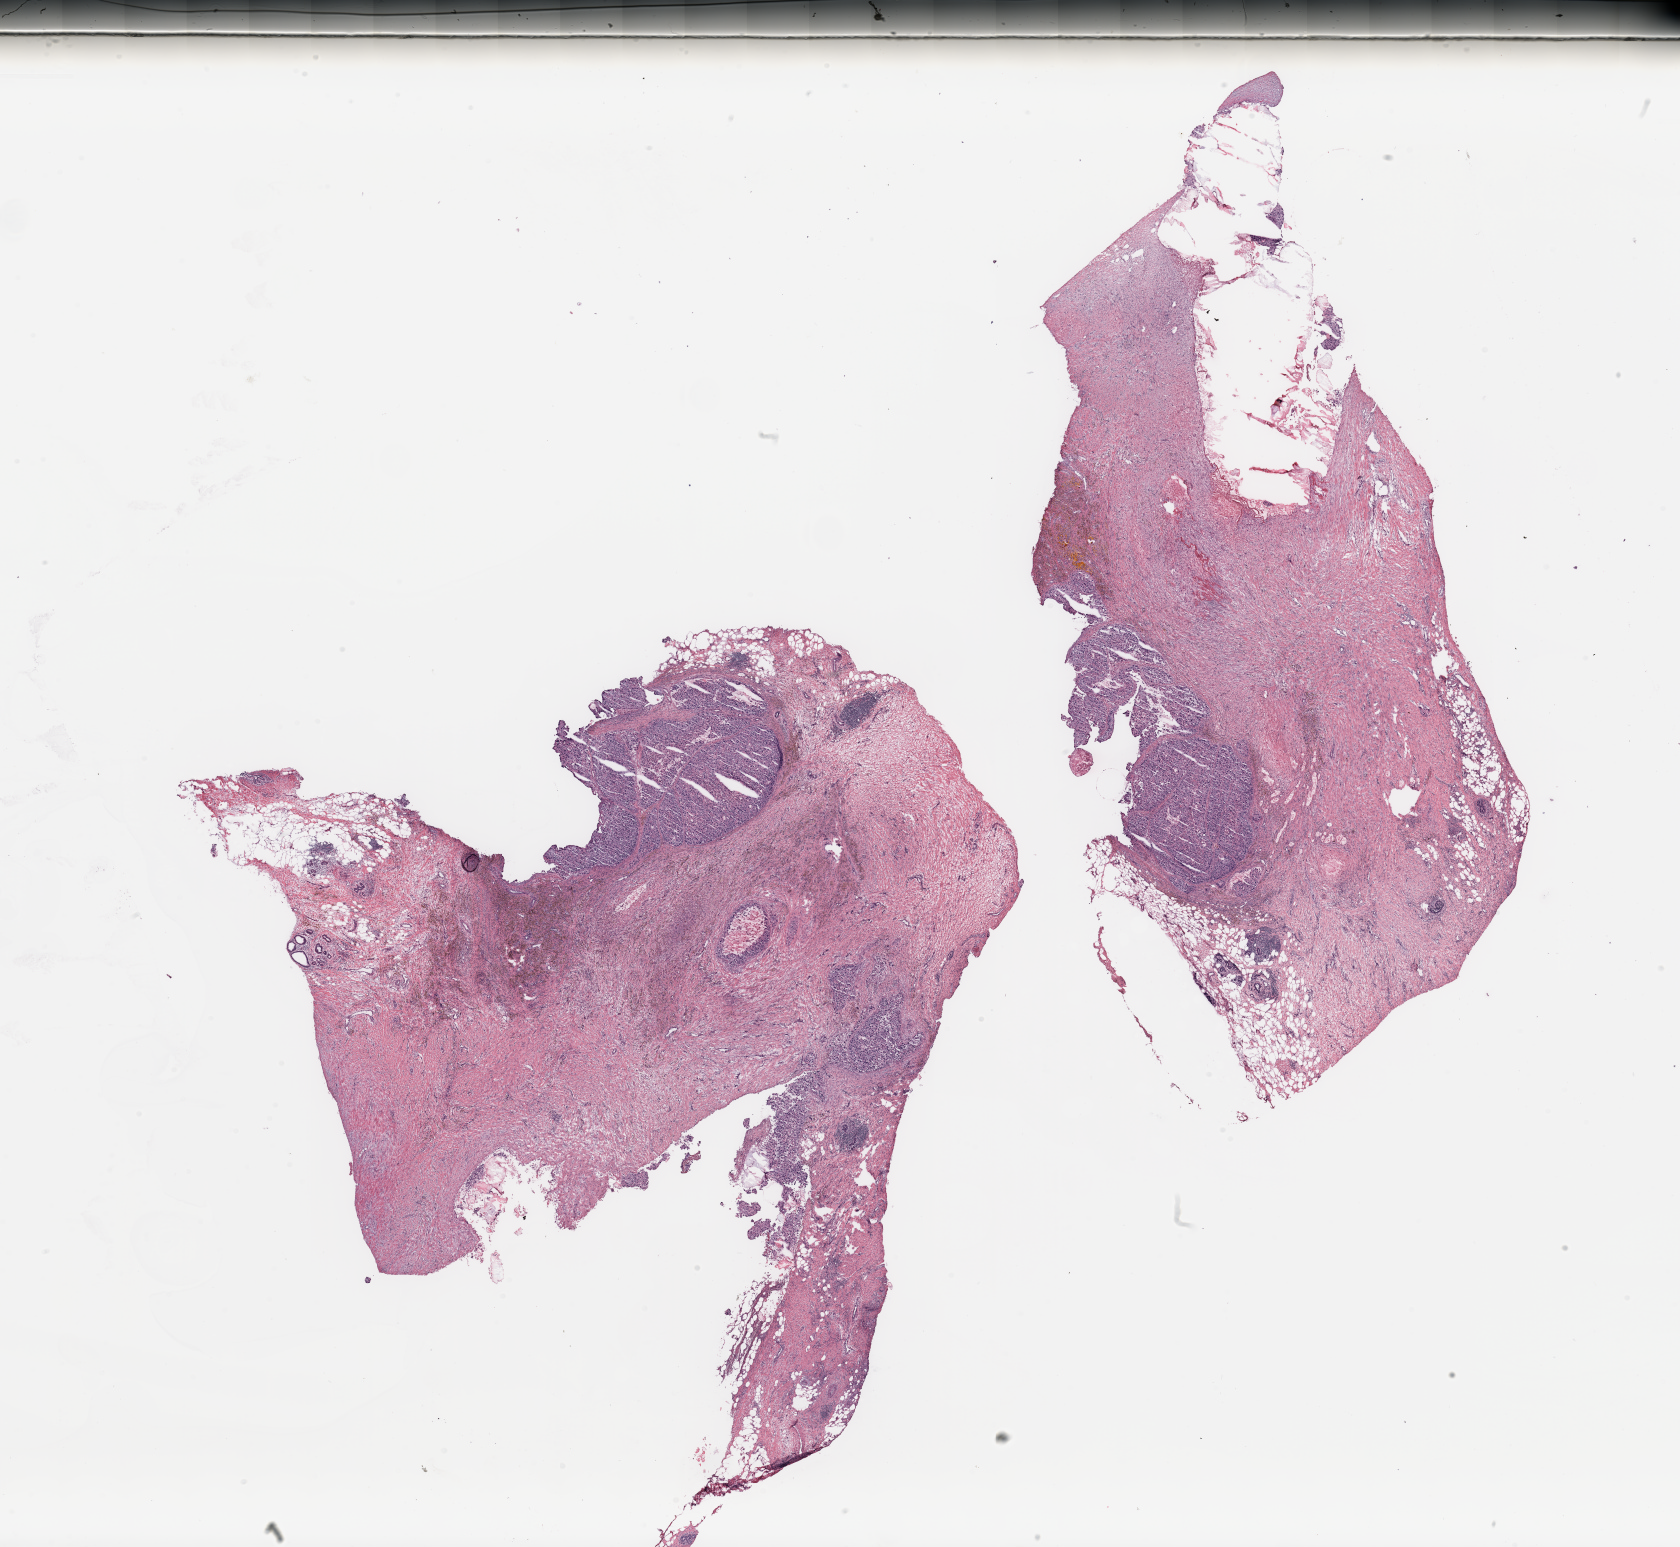
Digitized Hematoxylin and eosin (H&E) stained tissue section (whole slide) — whole scanned area (about 26.6 x 24.5 mm, from a 20x scan) shown as a low-resolution overview; breast, tissue type not recorded.
Patient diagnosis (cohort enrolment): breast cancer (breast).